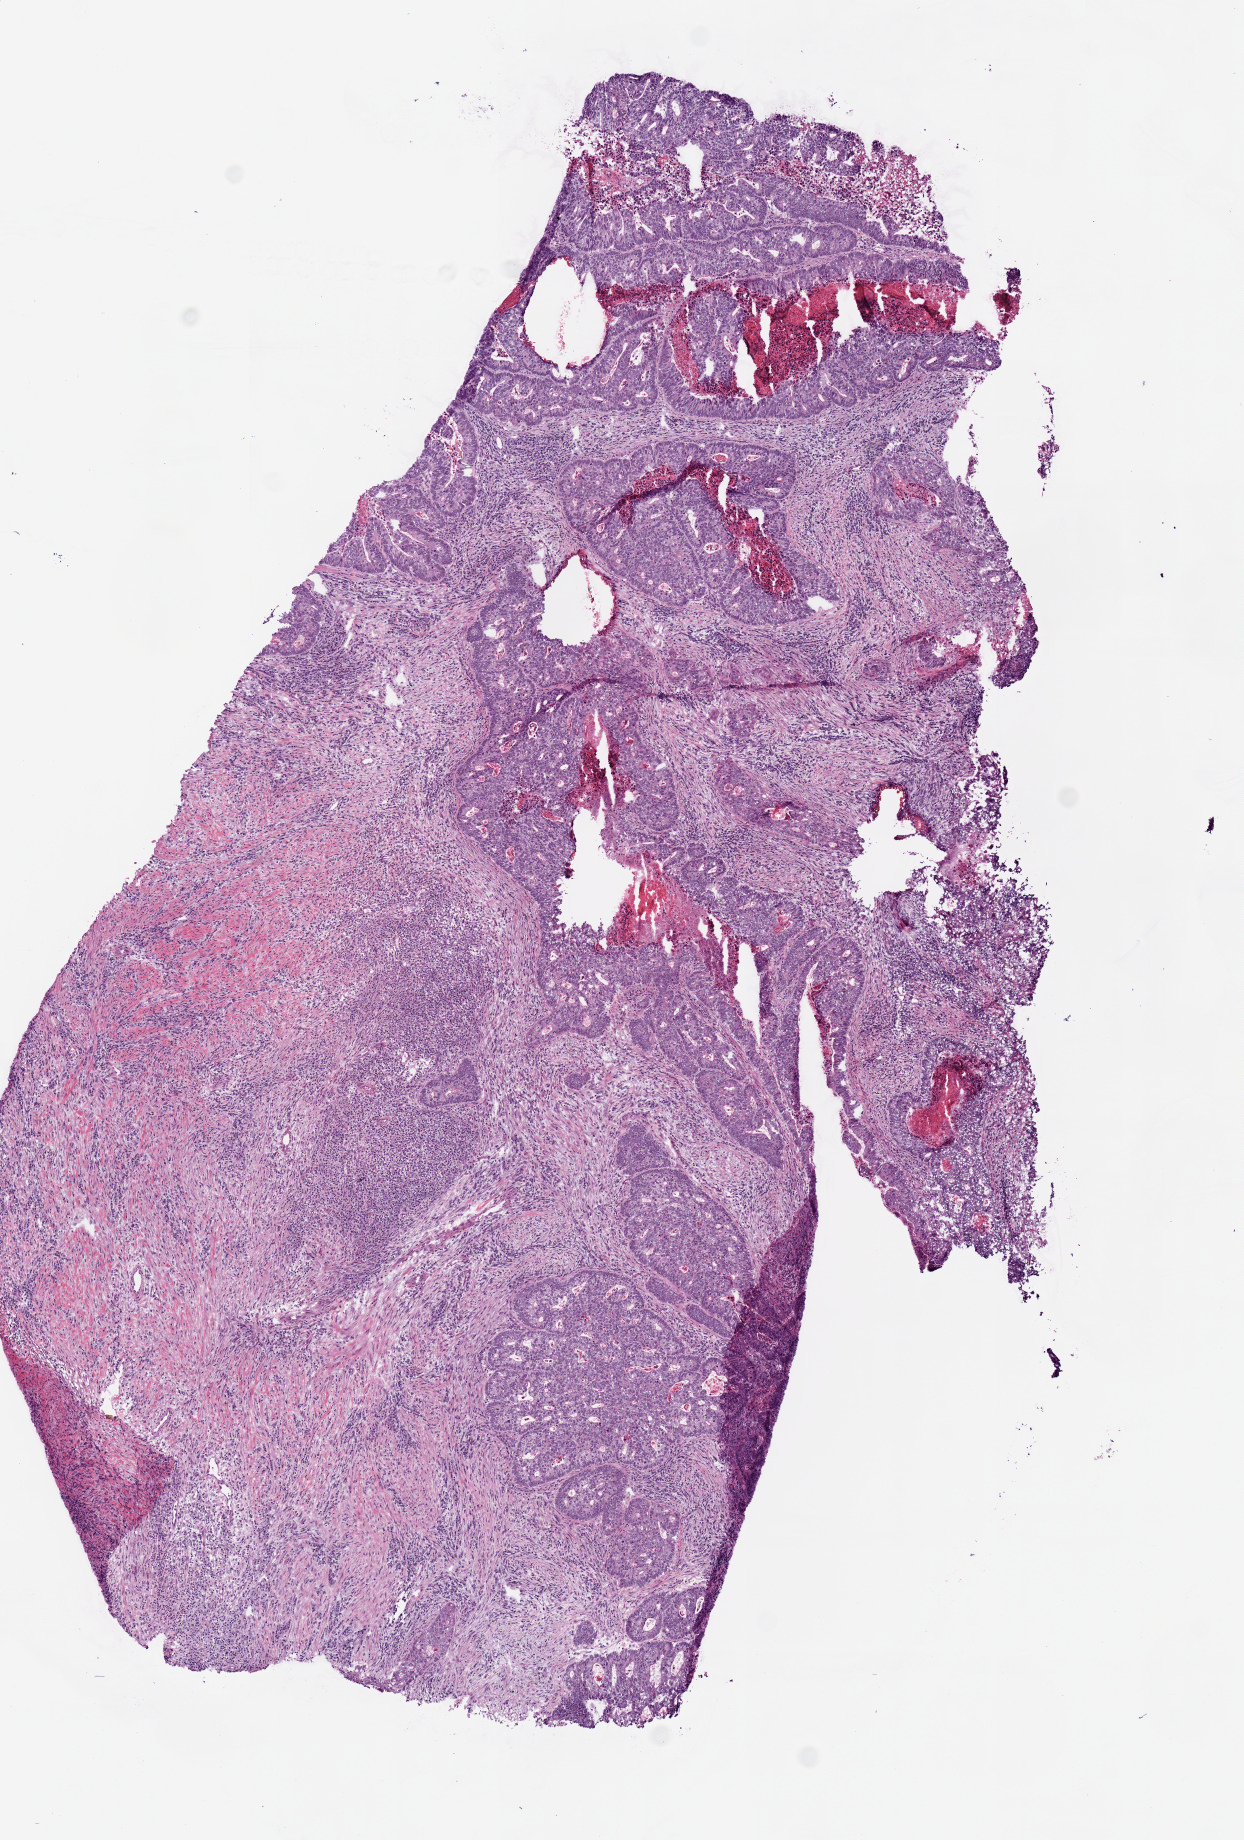
Whole-slide histology image, Hematoxylin and eosin (H&E) stained, shown as a low-resolution overview of the whole scanned area (about 4.9 x 7.3 mm). Frozen section. Colon, primary tumour sample. Patient: female, age at initial diagnosis 49 years. Slide review estimates, as recorded: tumour cells 70%, tumour nuclei 70%, normal cells 0%, stromal cells 10%, necrosis 20%.
- TNM: T3 N1 M1
- AJCC pathologic stage: IV (7th edition)
- pathologic diagnosis: Adenocarcinoma, NOS